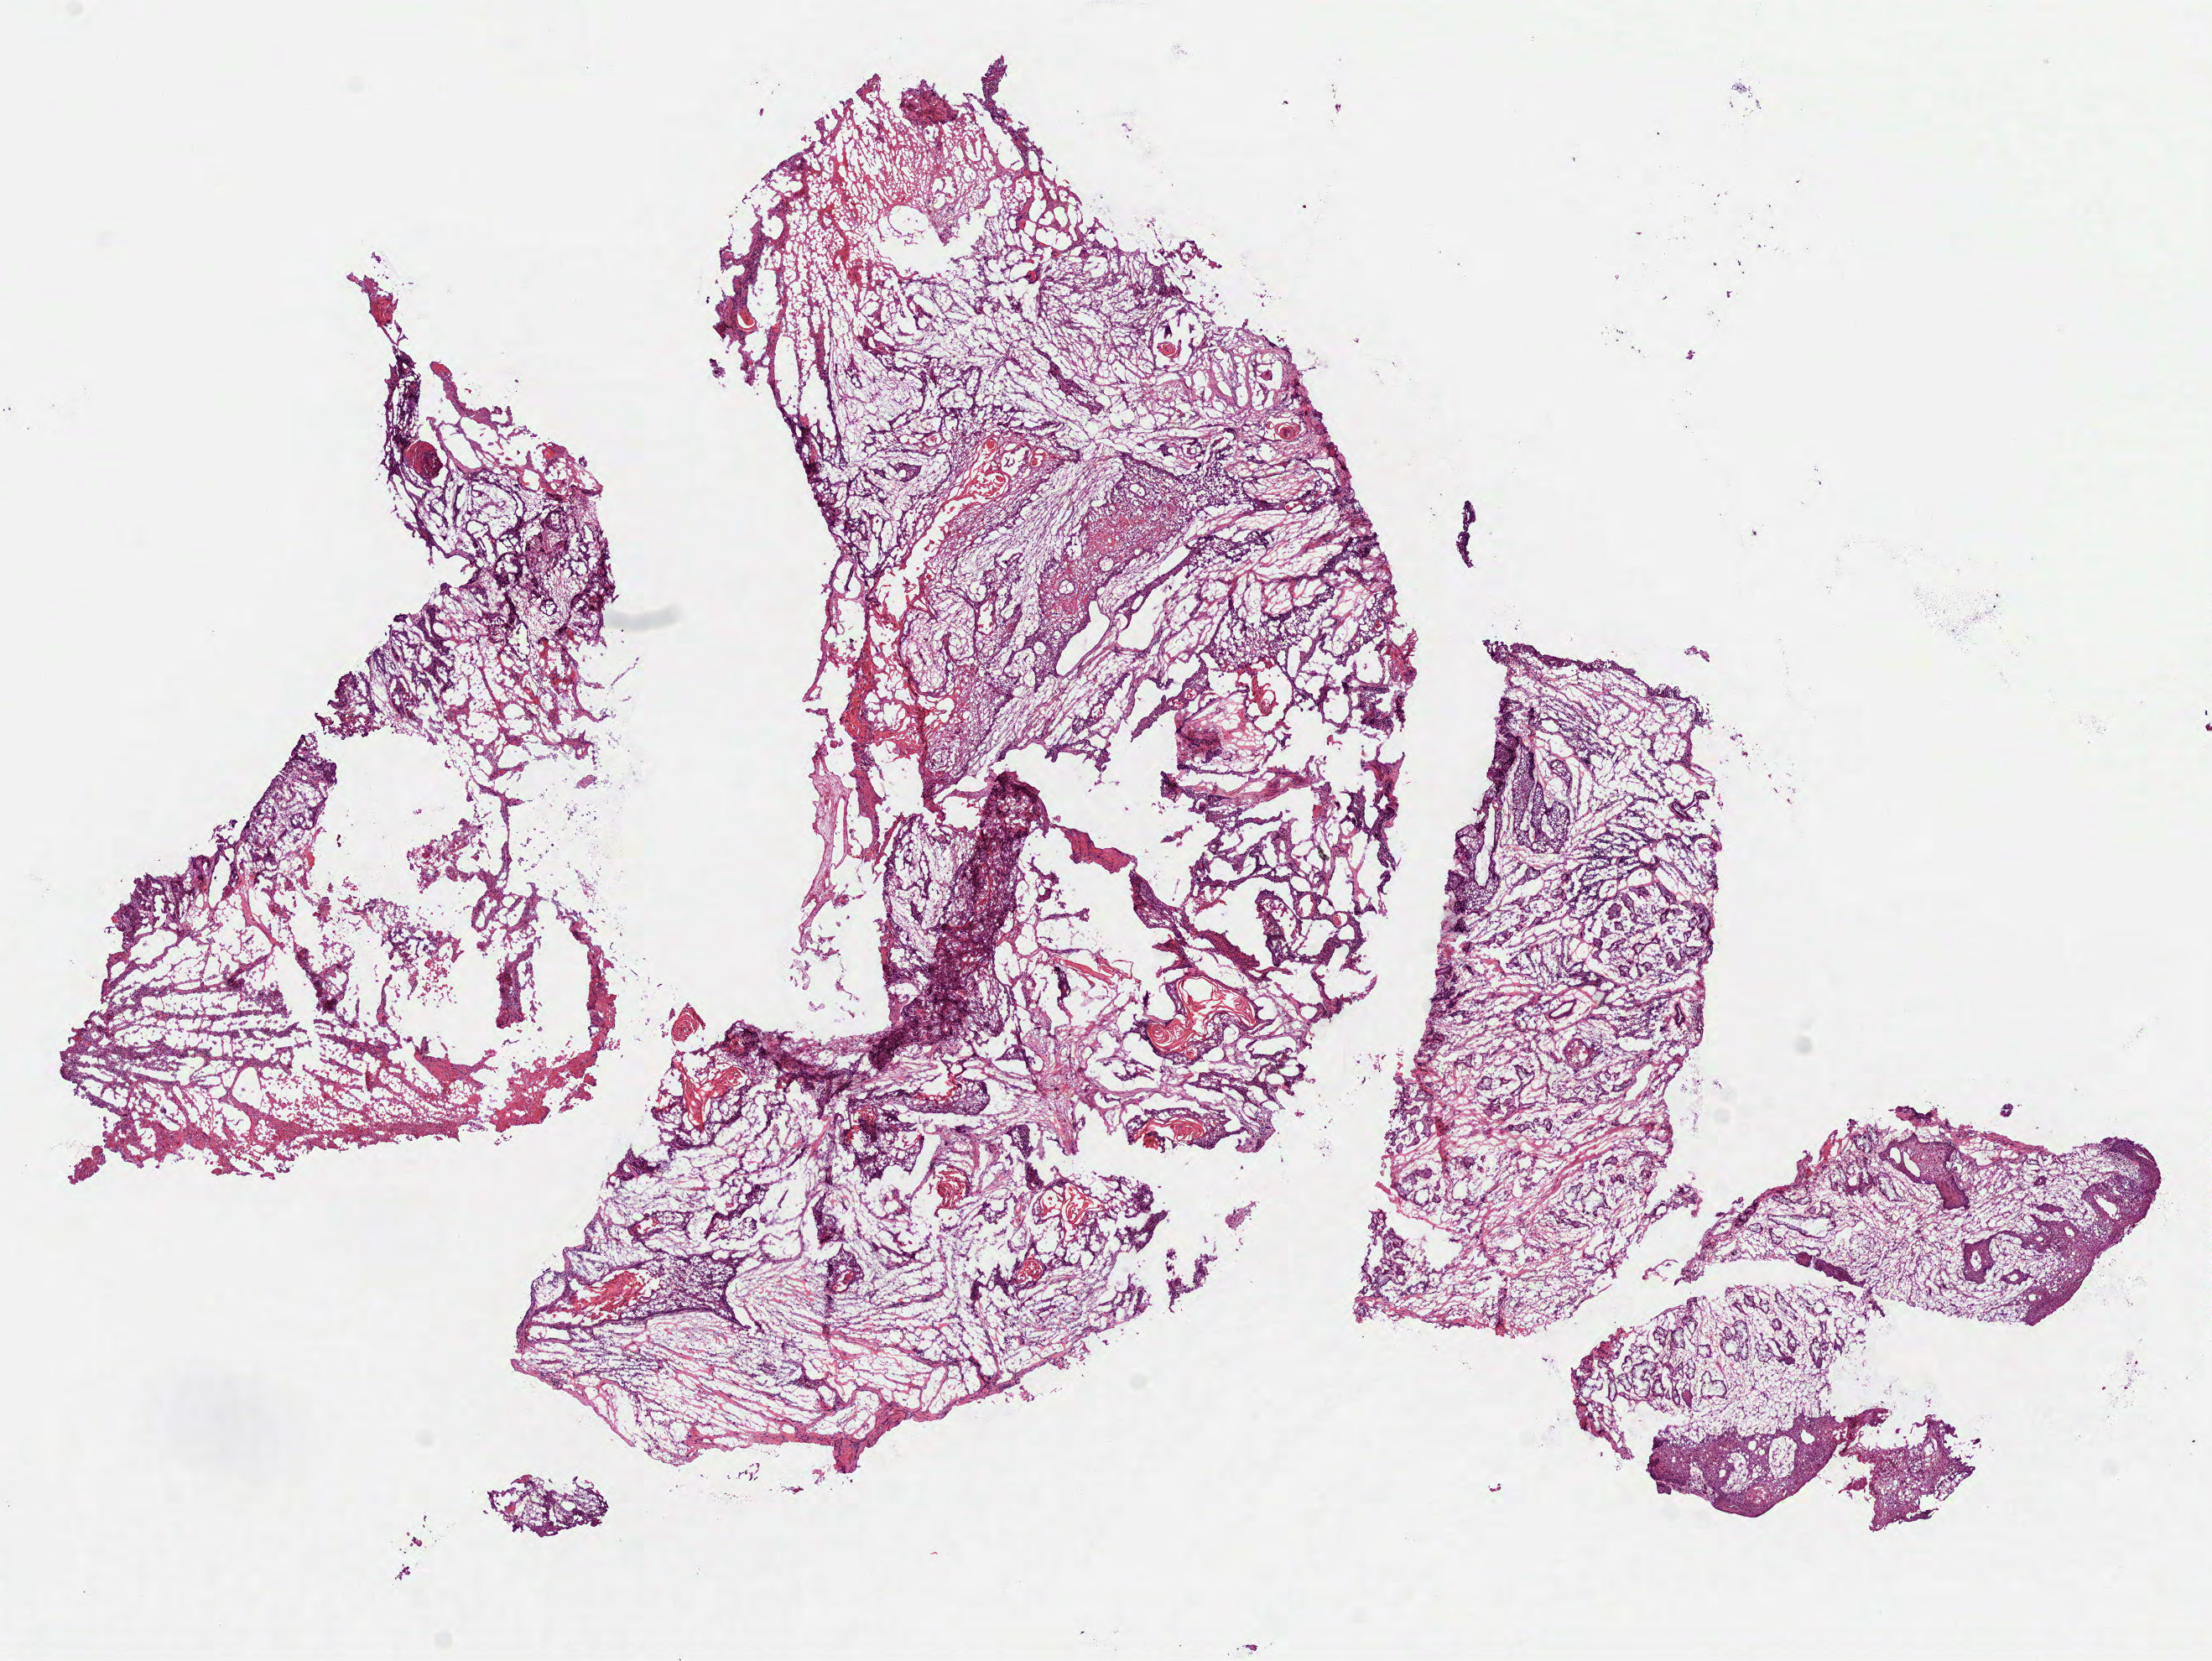
Whole-slide histology image, H&E — a low-resolution overview of the entire scanned area, about 10.6 x 8.0 mm (slide scanned at 40x); frozen section from the bottom of the tissue portion; sample: primary tumour, head and neck. Male patient; age at initial diagnosis 57 years. Histologic grade: G2 (moderately differentiated). Composition of this section per pathologist review: tumour cells 72%, tumour nuclei 65%, normal cells 8%, stromal cells 20%, necrosis 0%.
Histologic diagnosis: Squamous cell carcinoma, NOS (larynx, NOS). AJCC pathologic stage: IVA.